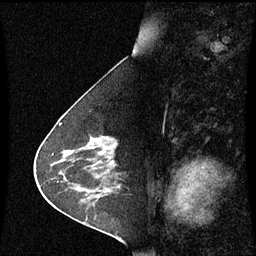
Breast MRI (dynamic contrast-enhanced), one sagittal slice; slice 29 of 60 in the series (ordered by position); dynamic contrast-enhanced series, image 2 of 3 at this slice position (ordered by acquisition); 1.5 T; TE 4.2 ms, TR 8.9 ms; 256 × 256 image matrix. Female patient, age 63 years. Case-level facts recorded for this patient, not image findings: setting: breast cancer imaged before/during neoadjuvant chemotherapy; receptor status: HR-positive, HER2-negative.
Annotated regions visible in this slice (semi-automatic segmentation, software-assisted and operator-edited):
- analysis volume of interest (the breast-tissue region the enhancement analysis was run in; not a lesion): bounding box [x1, y1, x2, y2] px = [76, 136, 123, 178]
- tumour enhancement mask (voxels above the 70 % enhancement threshold inside the analysis volume of interest): [105, 149, 114, 164]